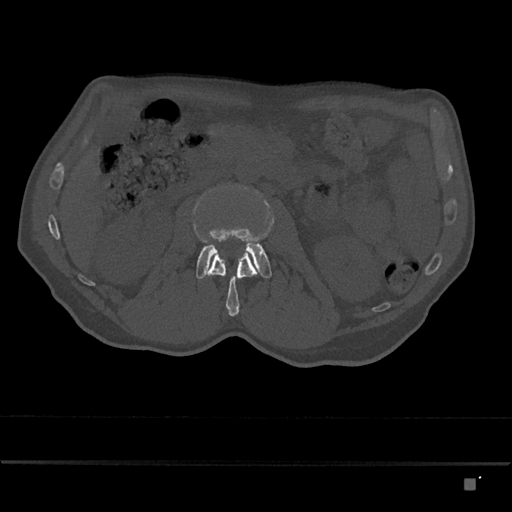
CT including the spine, one axial slice. Position 441 of 797 along the scan axis. 120 kVp. Bone window (W 1800 / L 400 HU). 0.5 mm slice thickness. 512 × 512 image matrix, field of view 390 × 390 mm. Patient: male, 72 years. From the clinical record (not read from this slice): primary cancer: prostate.
Annotated regions visible in this slice (semi-automatically segmented with operator editing):
- L2 vertebra: bounding box <204,250,257,317> (left, top, right, bottom; pixels)
- L3 vertebra: <196,186,272,279>